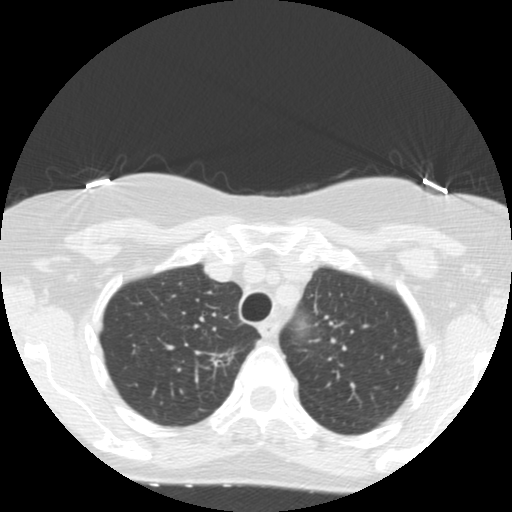
Low-dose screening chest CT, one axial slice. Position 121 of 155 along the scan axis. Reconstruction kernel STANDARD. 120 kVp. Lung window (W 1500 / L -600 HU). 2.5 mm slice thickness. 512 × 512 image matrix, field of view 300 × 300 mm.
Structures marked on this image (expert manual segmentation):
- lesion 1 (tumor, upper lobe of right lung): box from (x=210, y=352) to (x=234, y=368) px